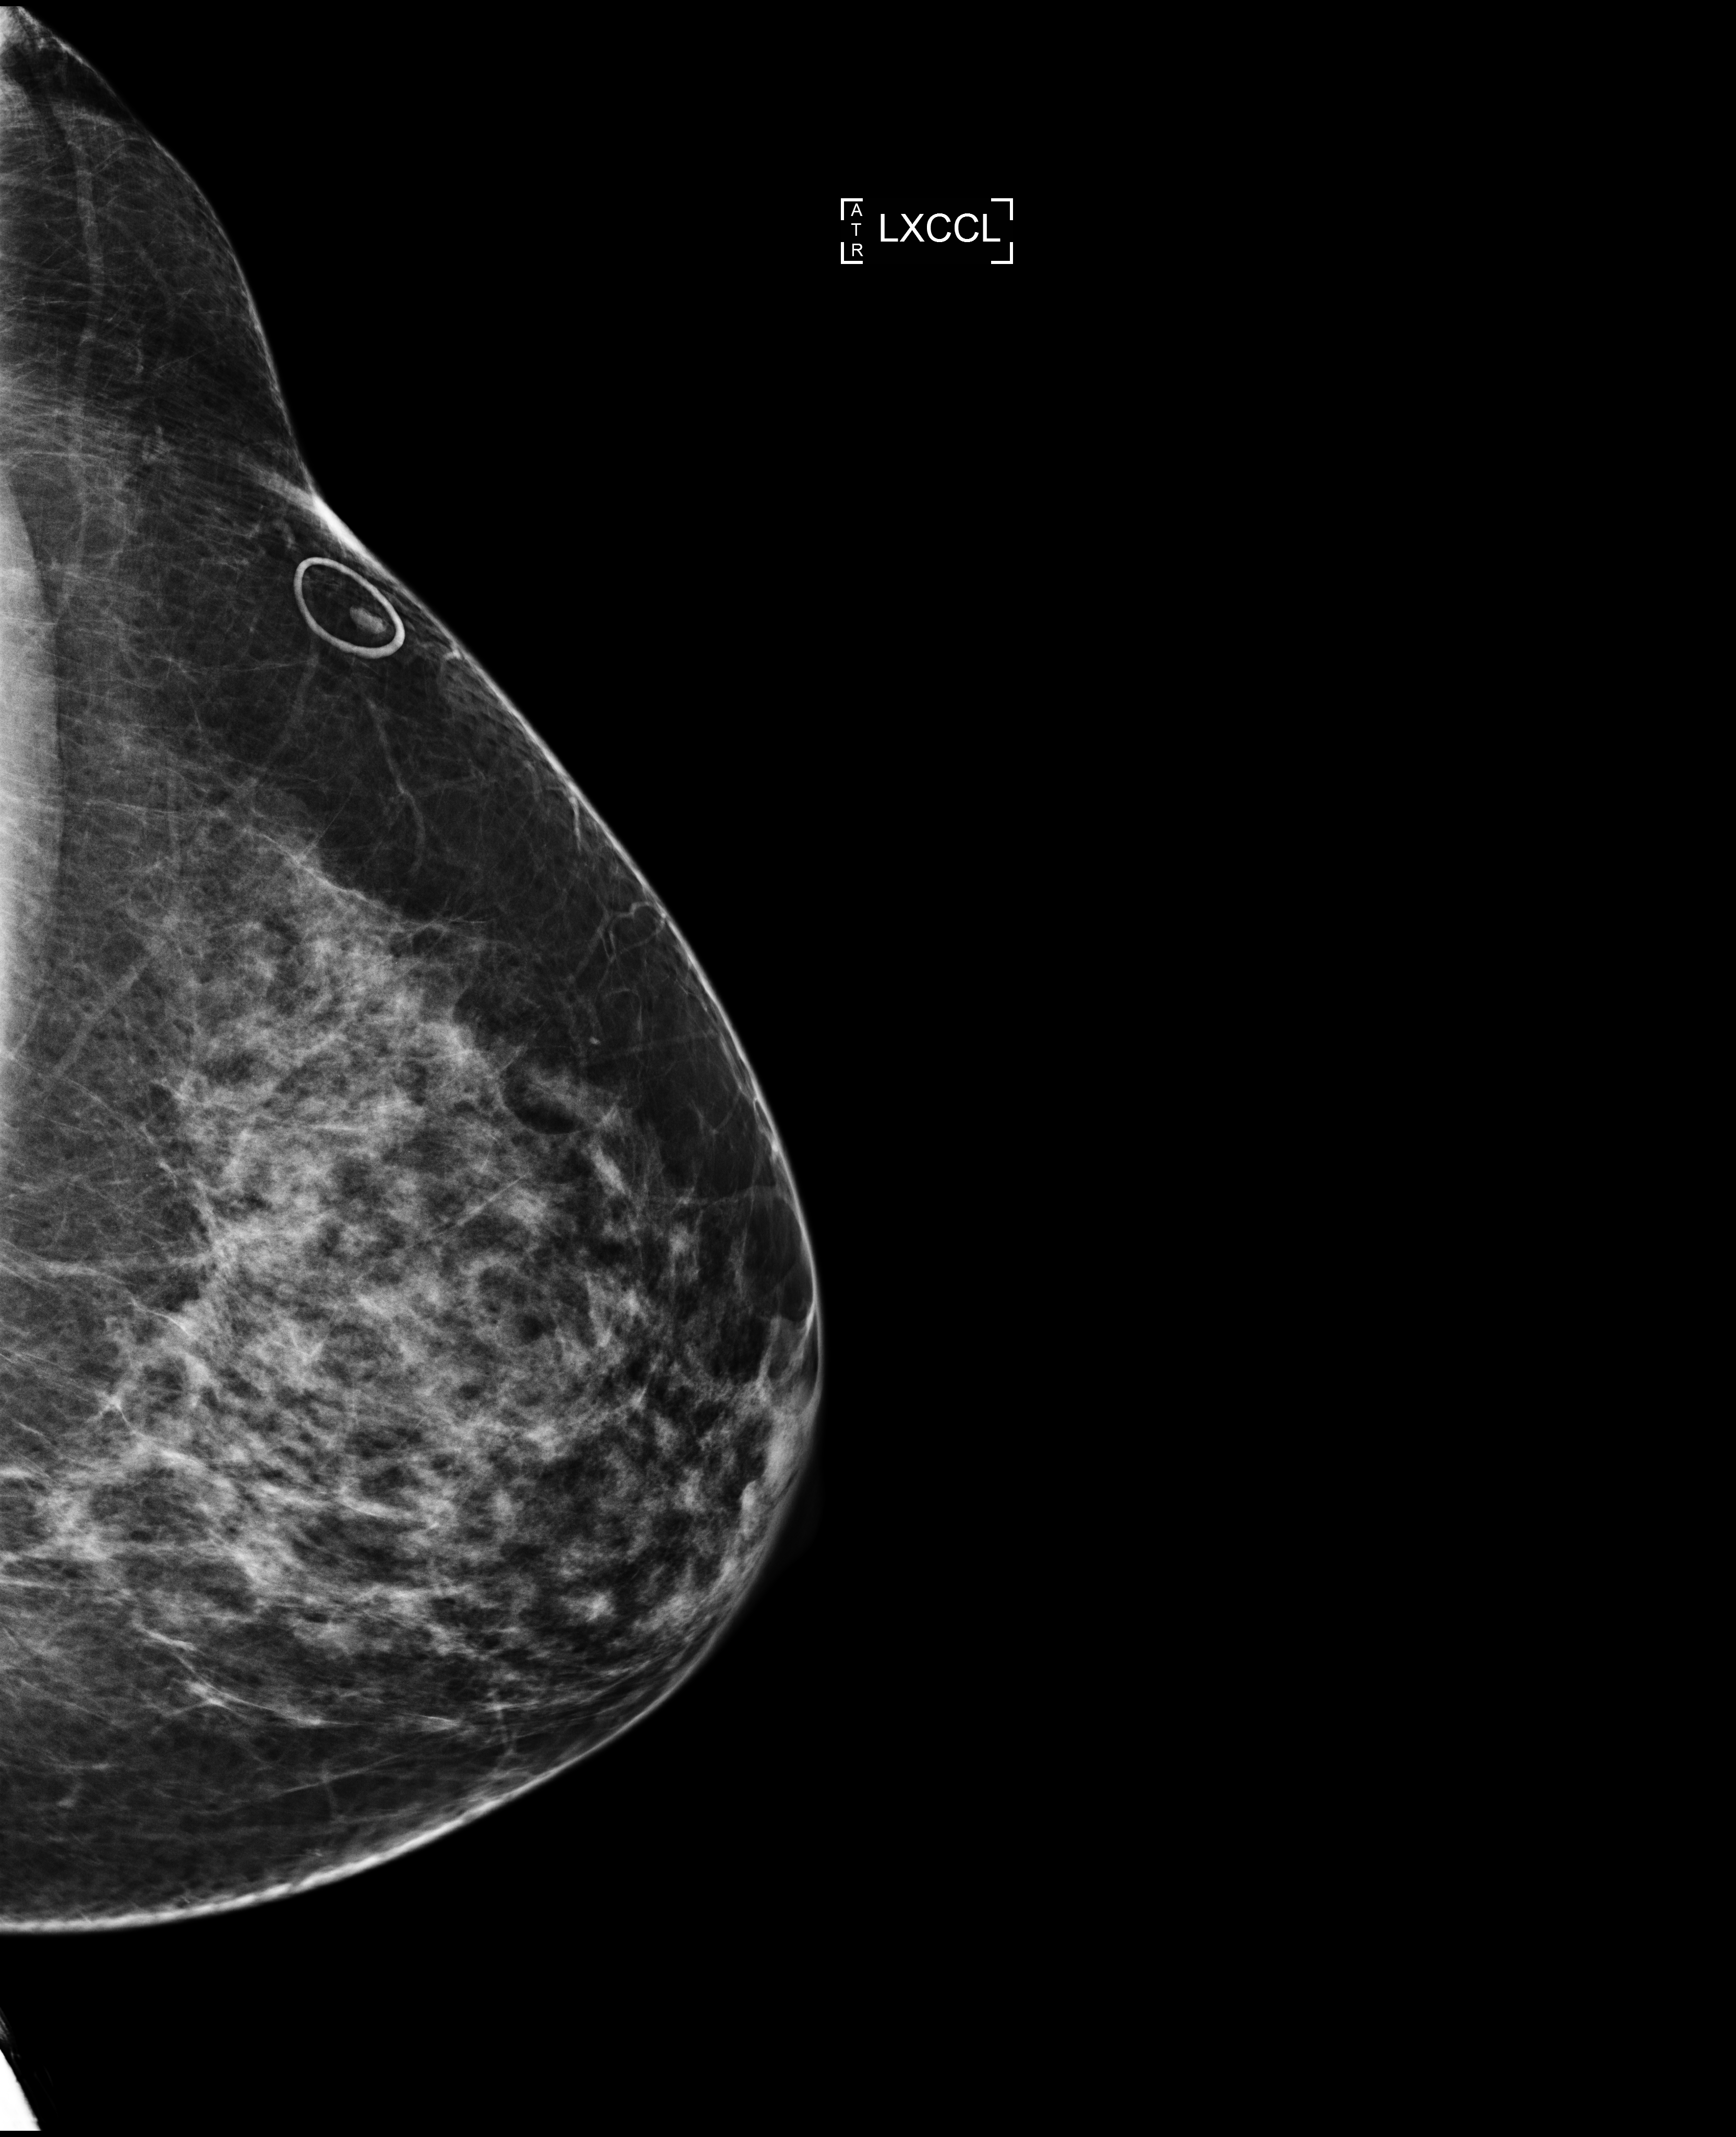
Annual screening mammography examination, compressed breast thickness 82 mm. Patient: female, 53 years.
Image type: full-field digital mammogram. Breast: left. Projection: exaggerated CC view (lateral).